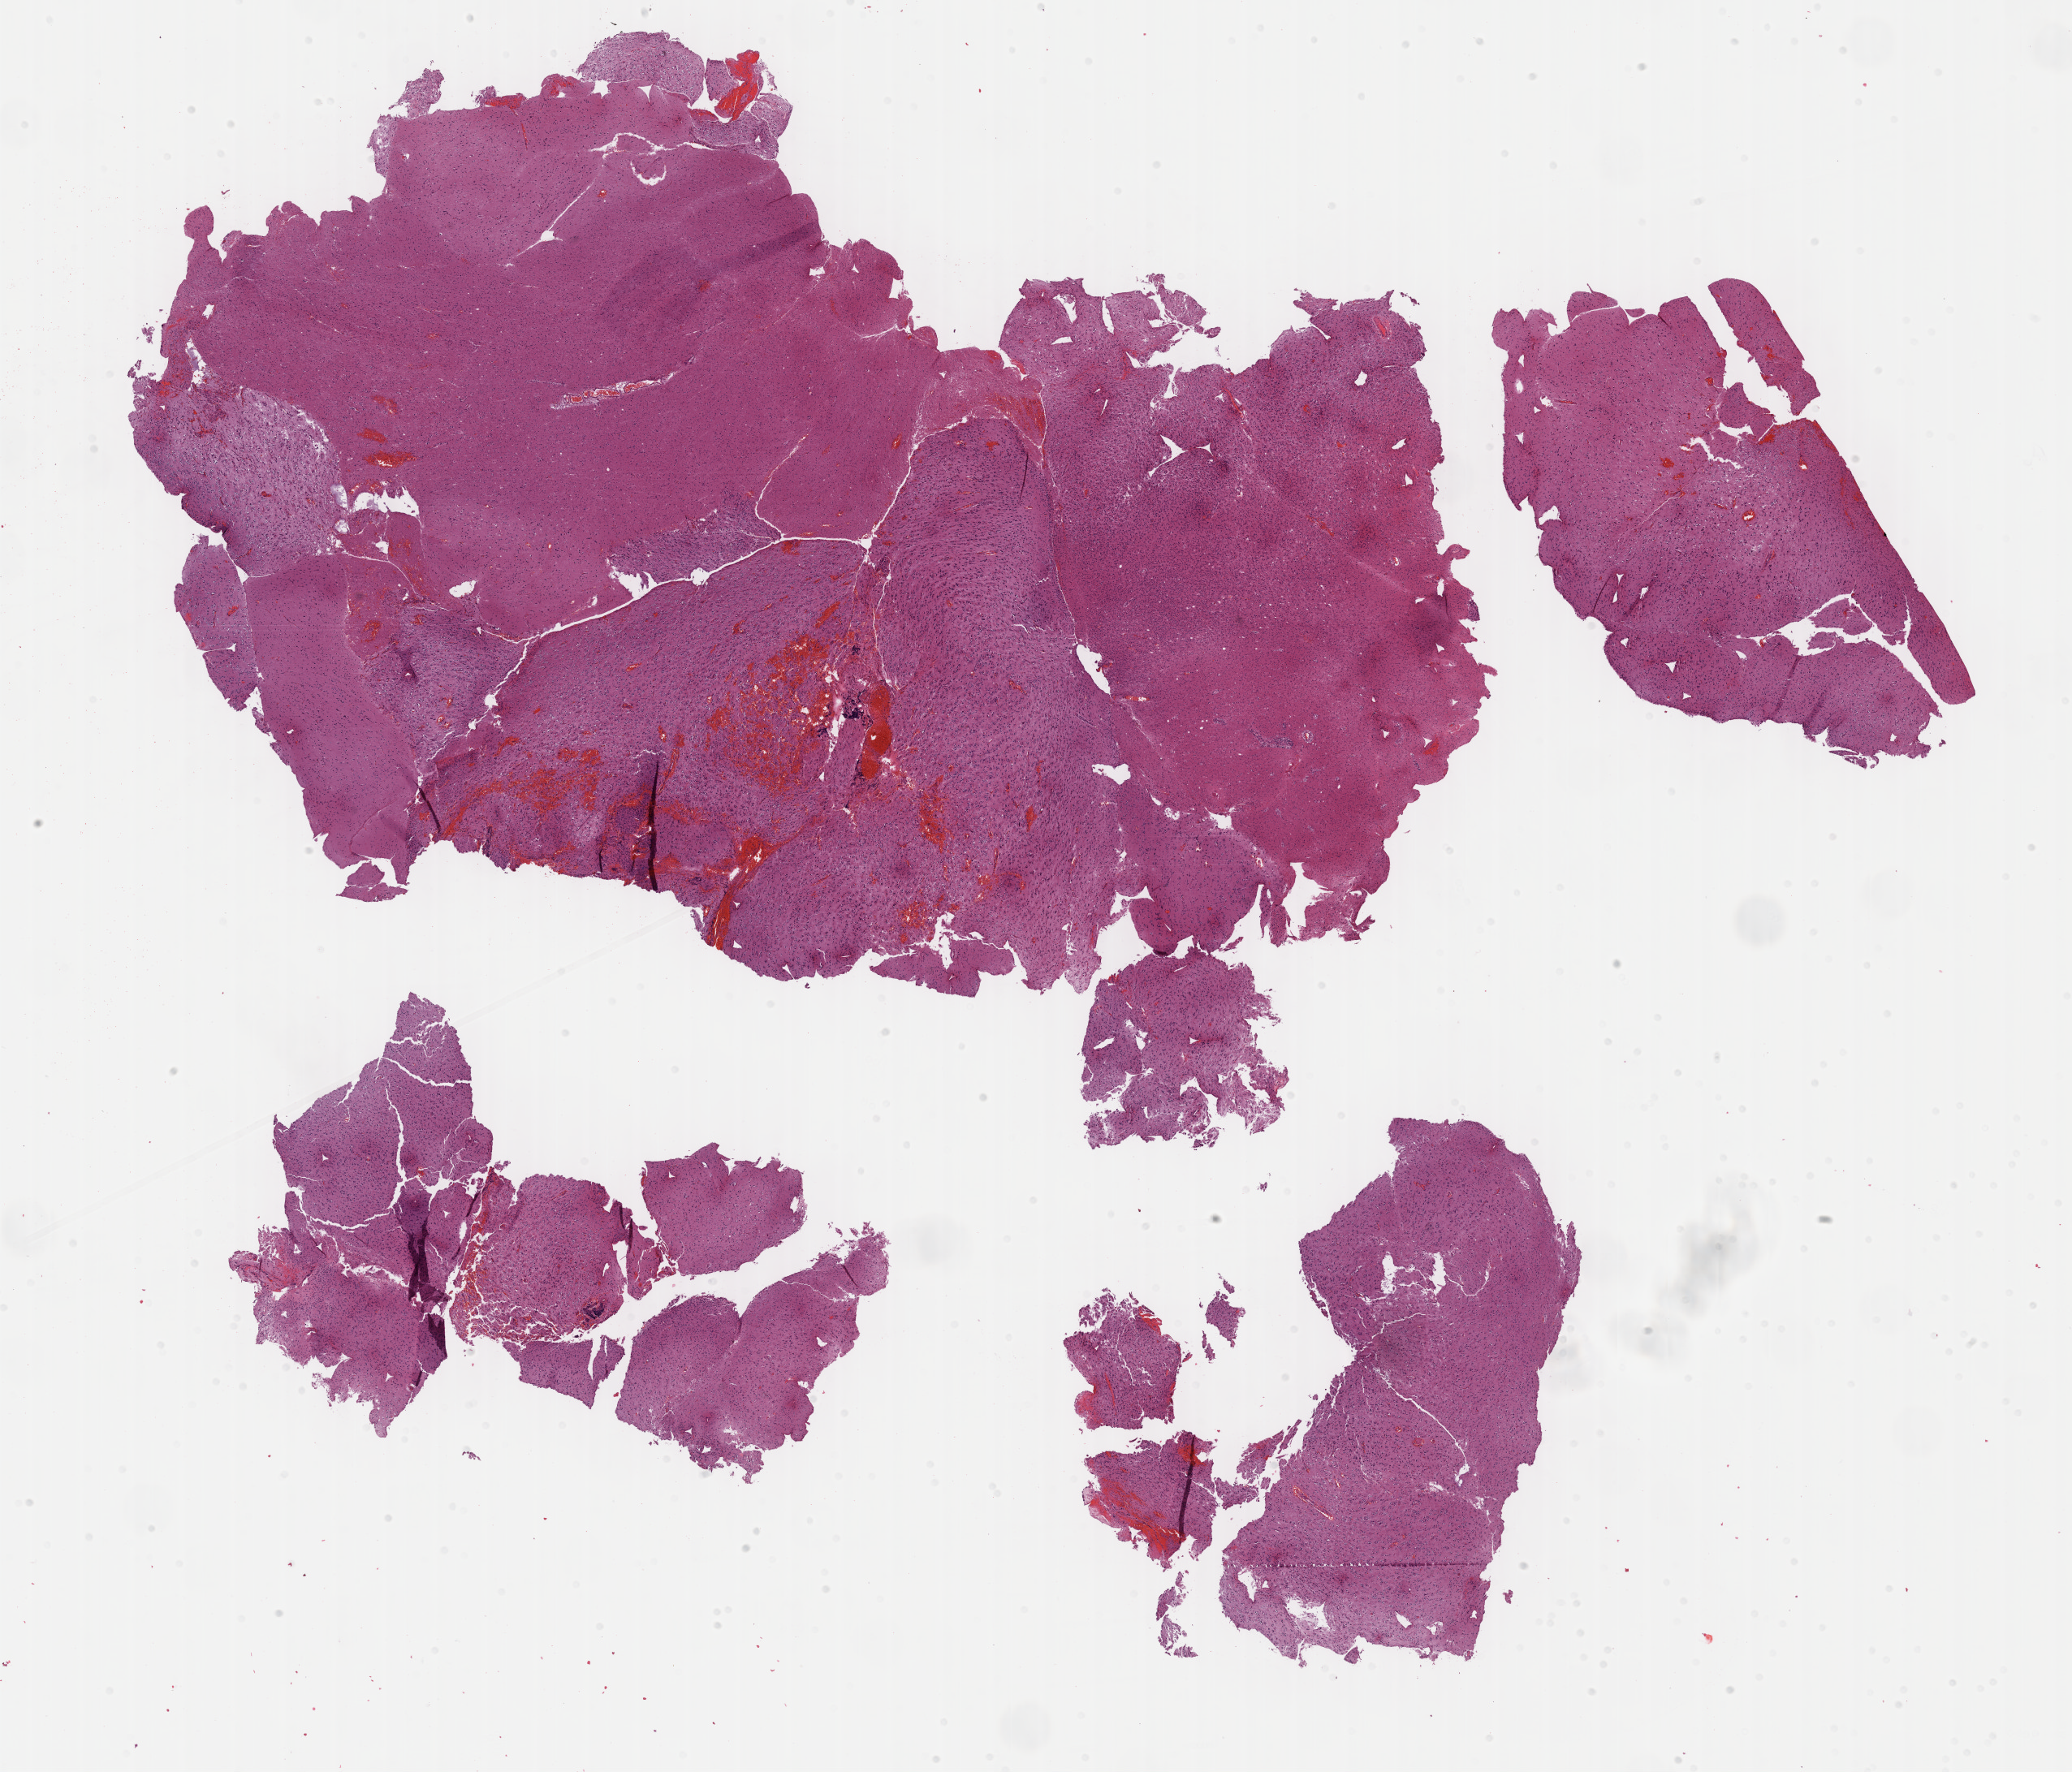
H&E-stained whole-slide image, low-resolution overview of the scanned area, about 20.6 x 17.7 mm (from a 40x scan); formalin-fixed paraffin-embedded (FFPE) diagnostic section; sample: primary tumour, brain. Male patient; age at initial diagnosis 54 years. Histologic grade: G2 (moderately differentiated).
Diagnosis: Oligodendroglioma, NOS. Laterality: right.